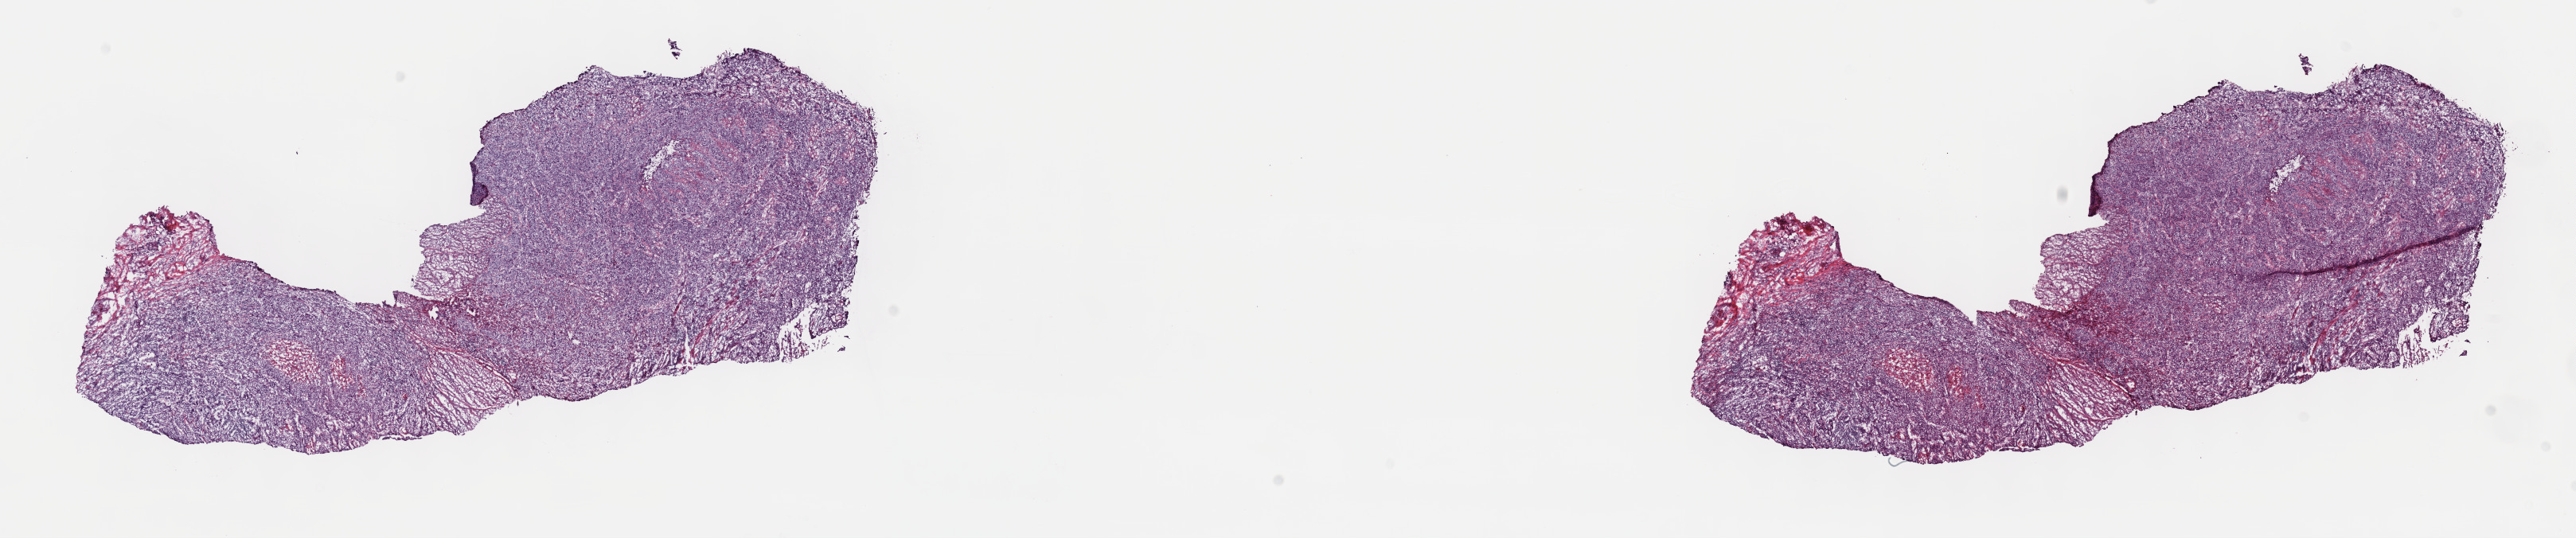
Digitized H&E tissue section (whole slide), low-resolution overview of the scanned area, about 26.2 x 5.5 mm (from a 40x scan); frozen section; bladder, primary tumour sample. Female, age 61 years at initial diagnosis. Histologic grade: high grade. Pathologist review of this section (percent, as recorded): tumour cells 67%, tumour nuclei 80%, normal cells 0%, stromal cells 18%, necrosis 15%. Infiltration values recorded for this section: lymphocyte infiltration 10%, monocyte infiltration 2%, neutrophil infiltration 2%.
Histologic diagnosis: Transitional cell carcinoma. AJCC pathologic stage: III (6th edition).